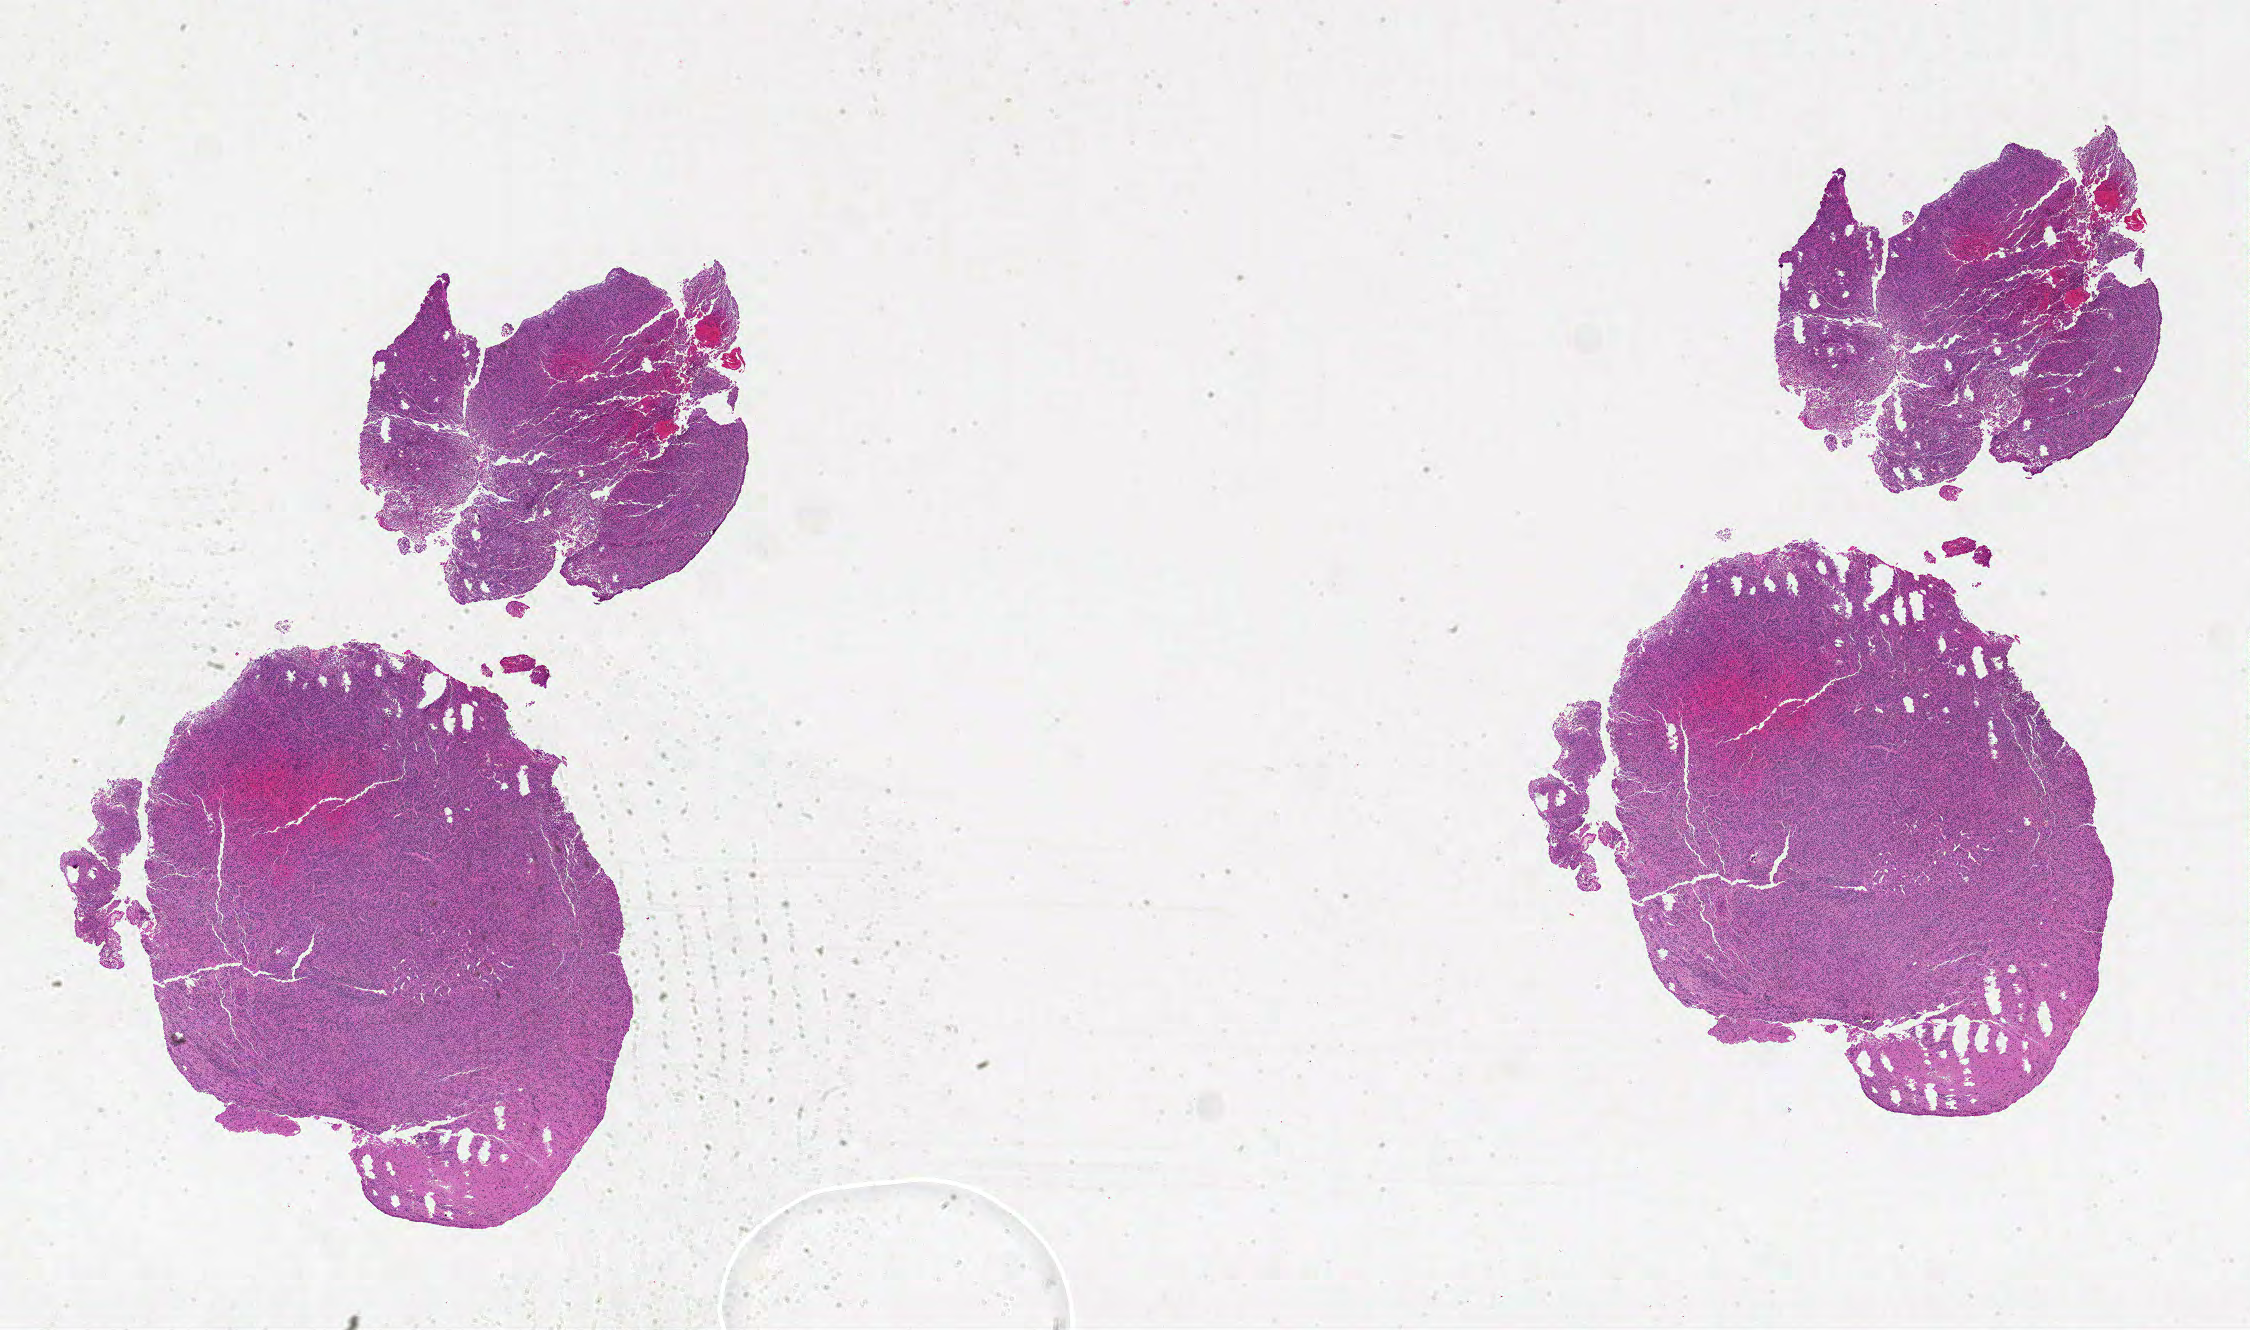
Whole-slide histology image, H&E, whole scanned area (about 36.0 x 21.3 mm, from a 20x scan) shown as a low-resolution overview; FFPE section; brain, primary tumour sample. Female, age 34 years at initial diagnosis.
* histologic diagnosis: Glioblastoma